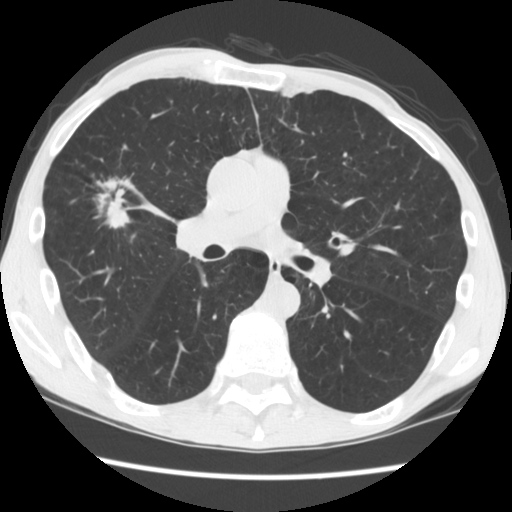
Chest CT (low-dose screening protocol), one axial image, second screening round (one year after baseline), lung window (W 1500 / L -600 HU), standard (soft-tissue) reconstruction kernel (STANDARD), 120 kVp, slice 85 of 181 in the series. Male, age 56 years at enrolment. Current smoker at enrolment.
- Lesion marked by an expert reader, box from (x=84, y=160) to (x=147, y=232) px.
- The screening reader recorded 2 non-calcified nodules or masses ≥4 mm on this exam; which of them this box marks is not recorded.
- Official screen result: positive, change unspecified: nodule(s) >= 4 mm or enlarging nodule(s), mass(es), or other non-specific abnormalities suspicious for lung cancer.
- Participant outcome: lung cancer diagnosed 101 days after this screen — squamous cell carcinoma, NOS, right upper lobe, right middle lobe, well differentiated (G1), stage IA (AJCC 6th edition), 27 mm at pathology.